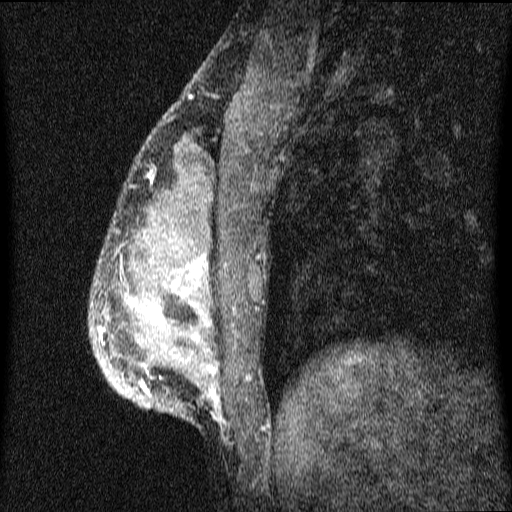
Breast MRI (dynamic contrast-enhanced), one sagittal slice. Position 20 of 64 along the scan axis. Dynamic contrast-enhanced series, image 2 of 4 at this slice position (ordered by acquisition). 1.5 T. TE 4.2 ms, TR 9.1 ms. 2 mm slice thickness. 512 × 512 image matrix, field of view 180 × 180 mm. Female patient, age 33 years.
Annotated regions visible in this slice (semi-automatic segmentation, software-assisted and operator-edited):
- analysis volume of interest (the breast-tissue region the enhancement analysis was run in; not a lesion): bounding box (x1, y1, x2, y2) in pixels: (90, 151, 335, 432)
- tumour enhancement mask (voxels above the 70 % enhancement threshold inside the analysis volume of interest): (99, 255, 223, 421)